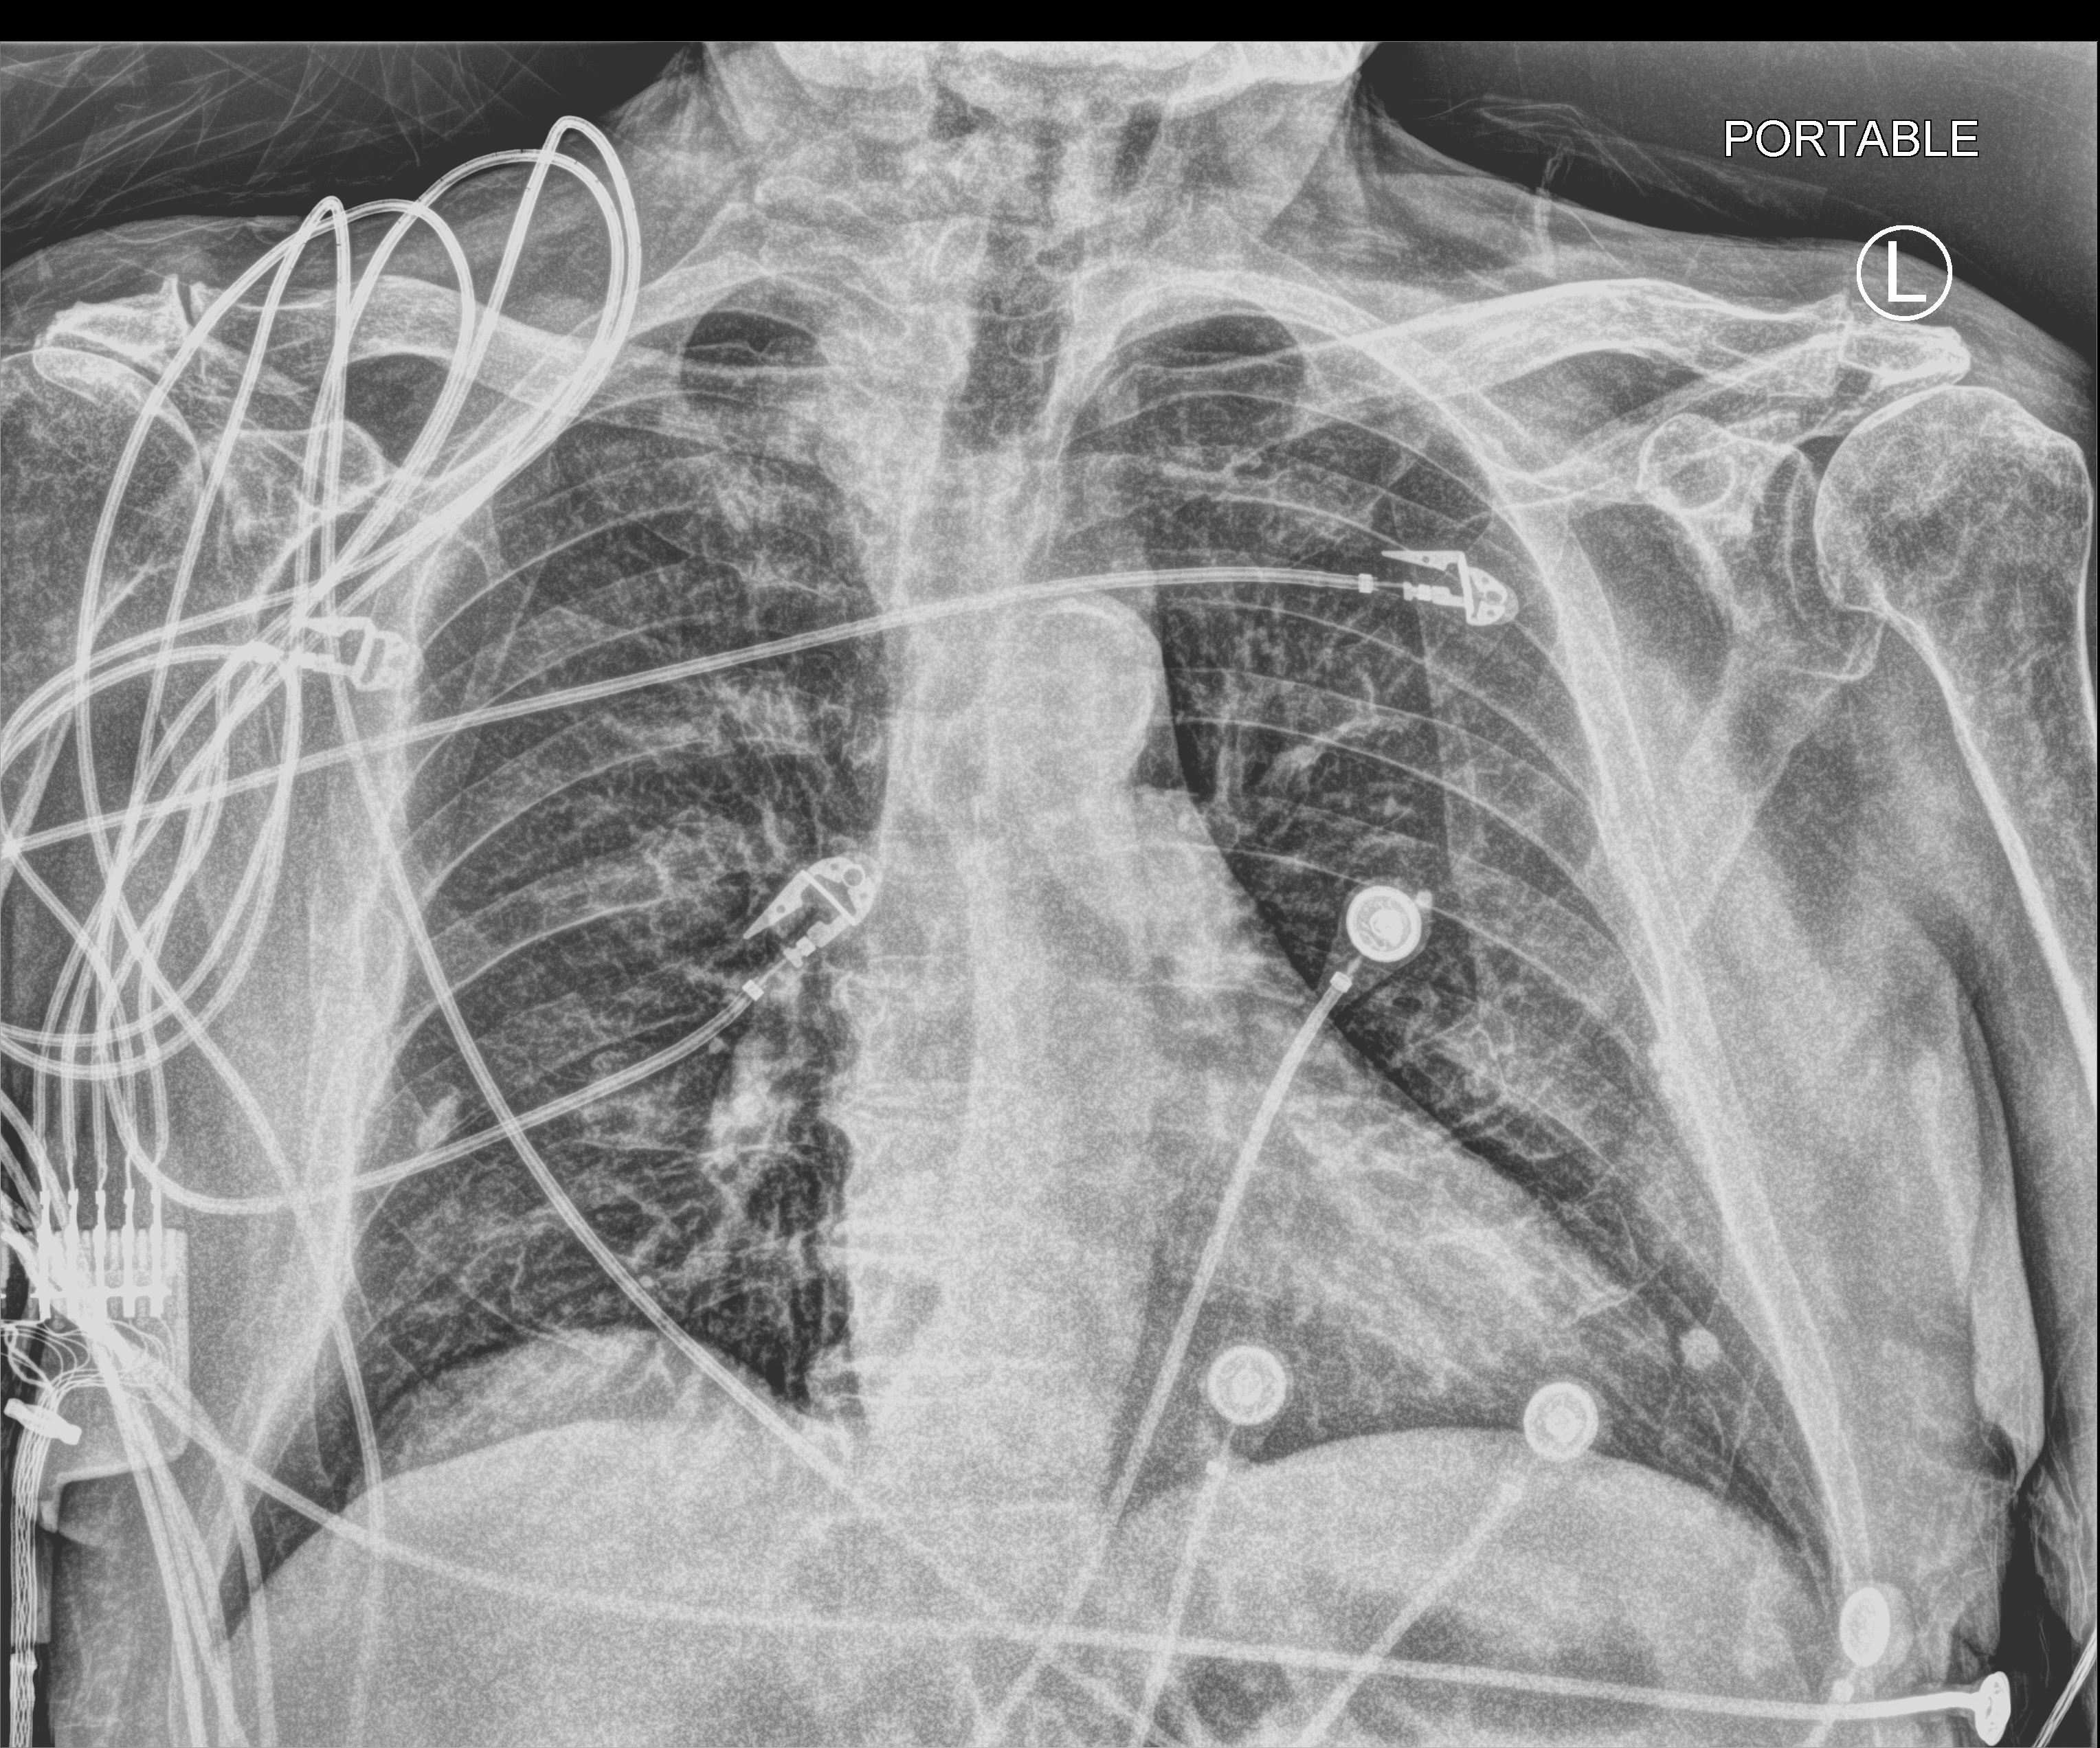
Bedside chest radiograph (computed radiography), anteroposterior (AP) projection. Patient hospitalised with COVID-19; male, aged 75–90 years.
From the hospital-stay record, not from the radiograph (when in the stay this image was taken is not recorded):
- hypertension (admission record): yes
- admitted to intensive care during this hospital stay: no
- other chronic lung disease (admission record): no